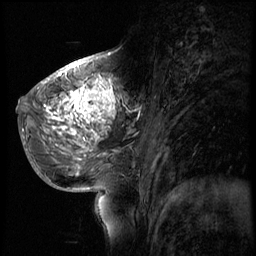
Breast MRI (dynamic contrast-enhanced), one sagittal slice. Slice 27 of 56 in the series (ordered by position). 4 images stored at this slice position (order not interpretable as contrast timing). 1.5 T. TE 4.2 ms, TR 8.9 ms. 2.5 mm slice thickness. 256 × 256 image matrix. Patient: female, 51 years. From the clinical record (not read from this slice): setting: breast cancer imaged before/during neoadjuvant chemotherapy; receptor status: triple-negative.
Structures marked on this image (semi-automatic segmentation, software-assisted and operator-edited):
- analysis volume of interest (the breast-tissue region the enhancement analysis was run in; not a lesion): box from (x=30, y=70) to (x=150, y=173) px
- tumour enhancement mask (voxels above the 140 % enhancement threshold inside the analysis volume of interest): (x=45, y=74)–(x=118, y=139)